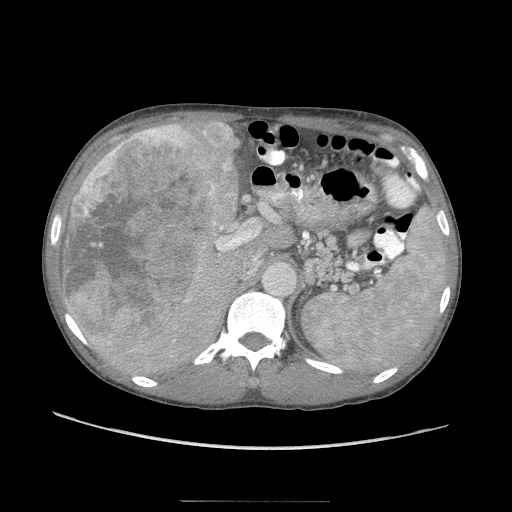
Contrast-enhanced abdominal CT (liver protocol), one axial slice; position 57 of 103 along the scan axis; reconstruction kernel STANDARD; 120 kVp; soft-tissue window (W 400 / L 40 HU); 512 × 512 image matrix, field of view 380 × 380 mm. From the clinical record (not read from this slice): diagnosis: hepatocellular carcinoma (patient treated with transarterial chemoembolisation; whether this scan precedes or follows treatment is not stated here); TNM stage (as recorded): Stage-IIIA; Child-Pugh class: A; tumour differentiation: moderately differentiated; tumour nodularity: multinodular.
Outlined on this slice (semi-automatically segmented with operator editing):
- liver parenchyma outside the tumour (the mass and vessels are separate outlines, so this box may not span the whole liver): bounding box (x1, y1, x2, y2) in pixels: (60, 120, 262, 376)
- mass: (62, 120, 237, 344)
- liver vessels: (213, 191, 215, 194)